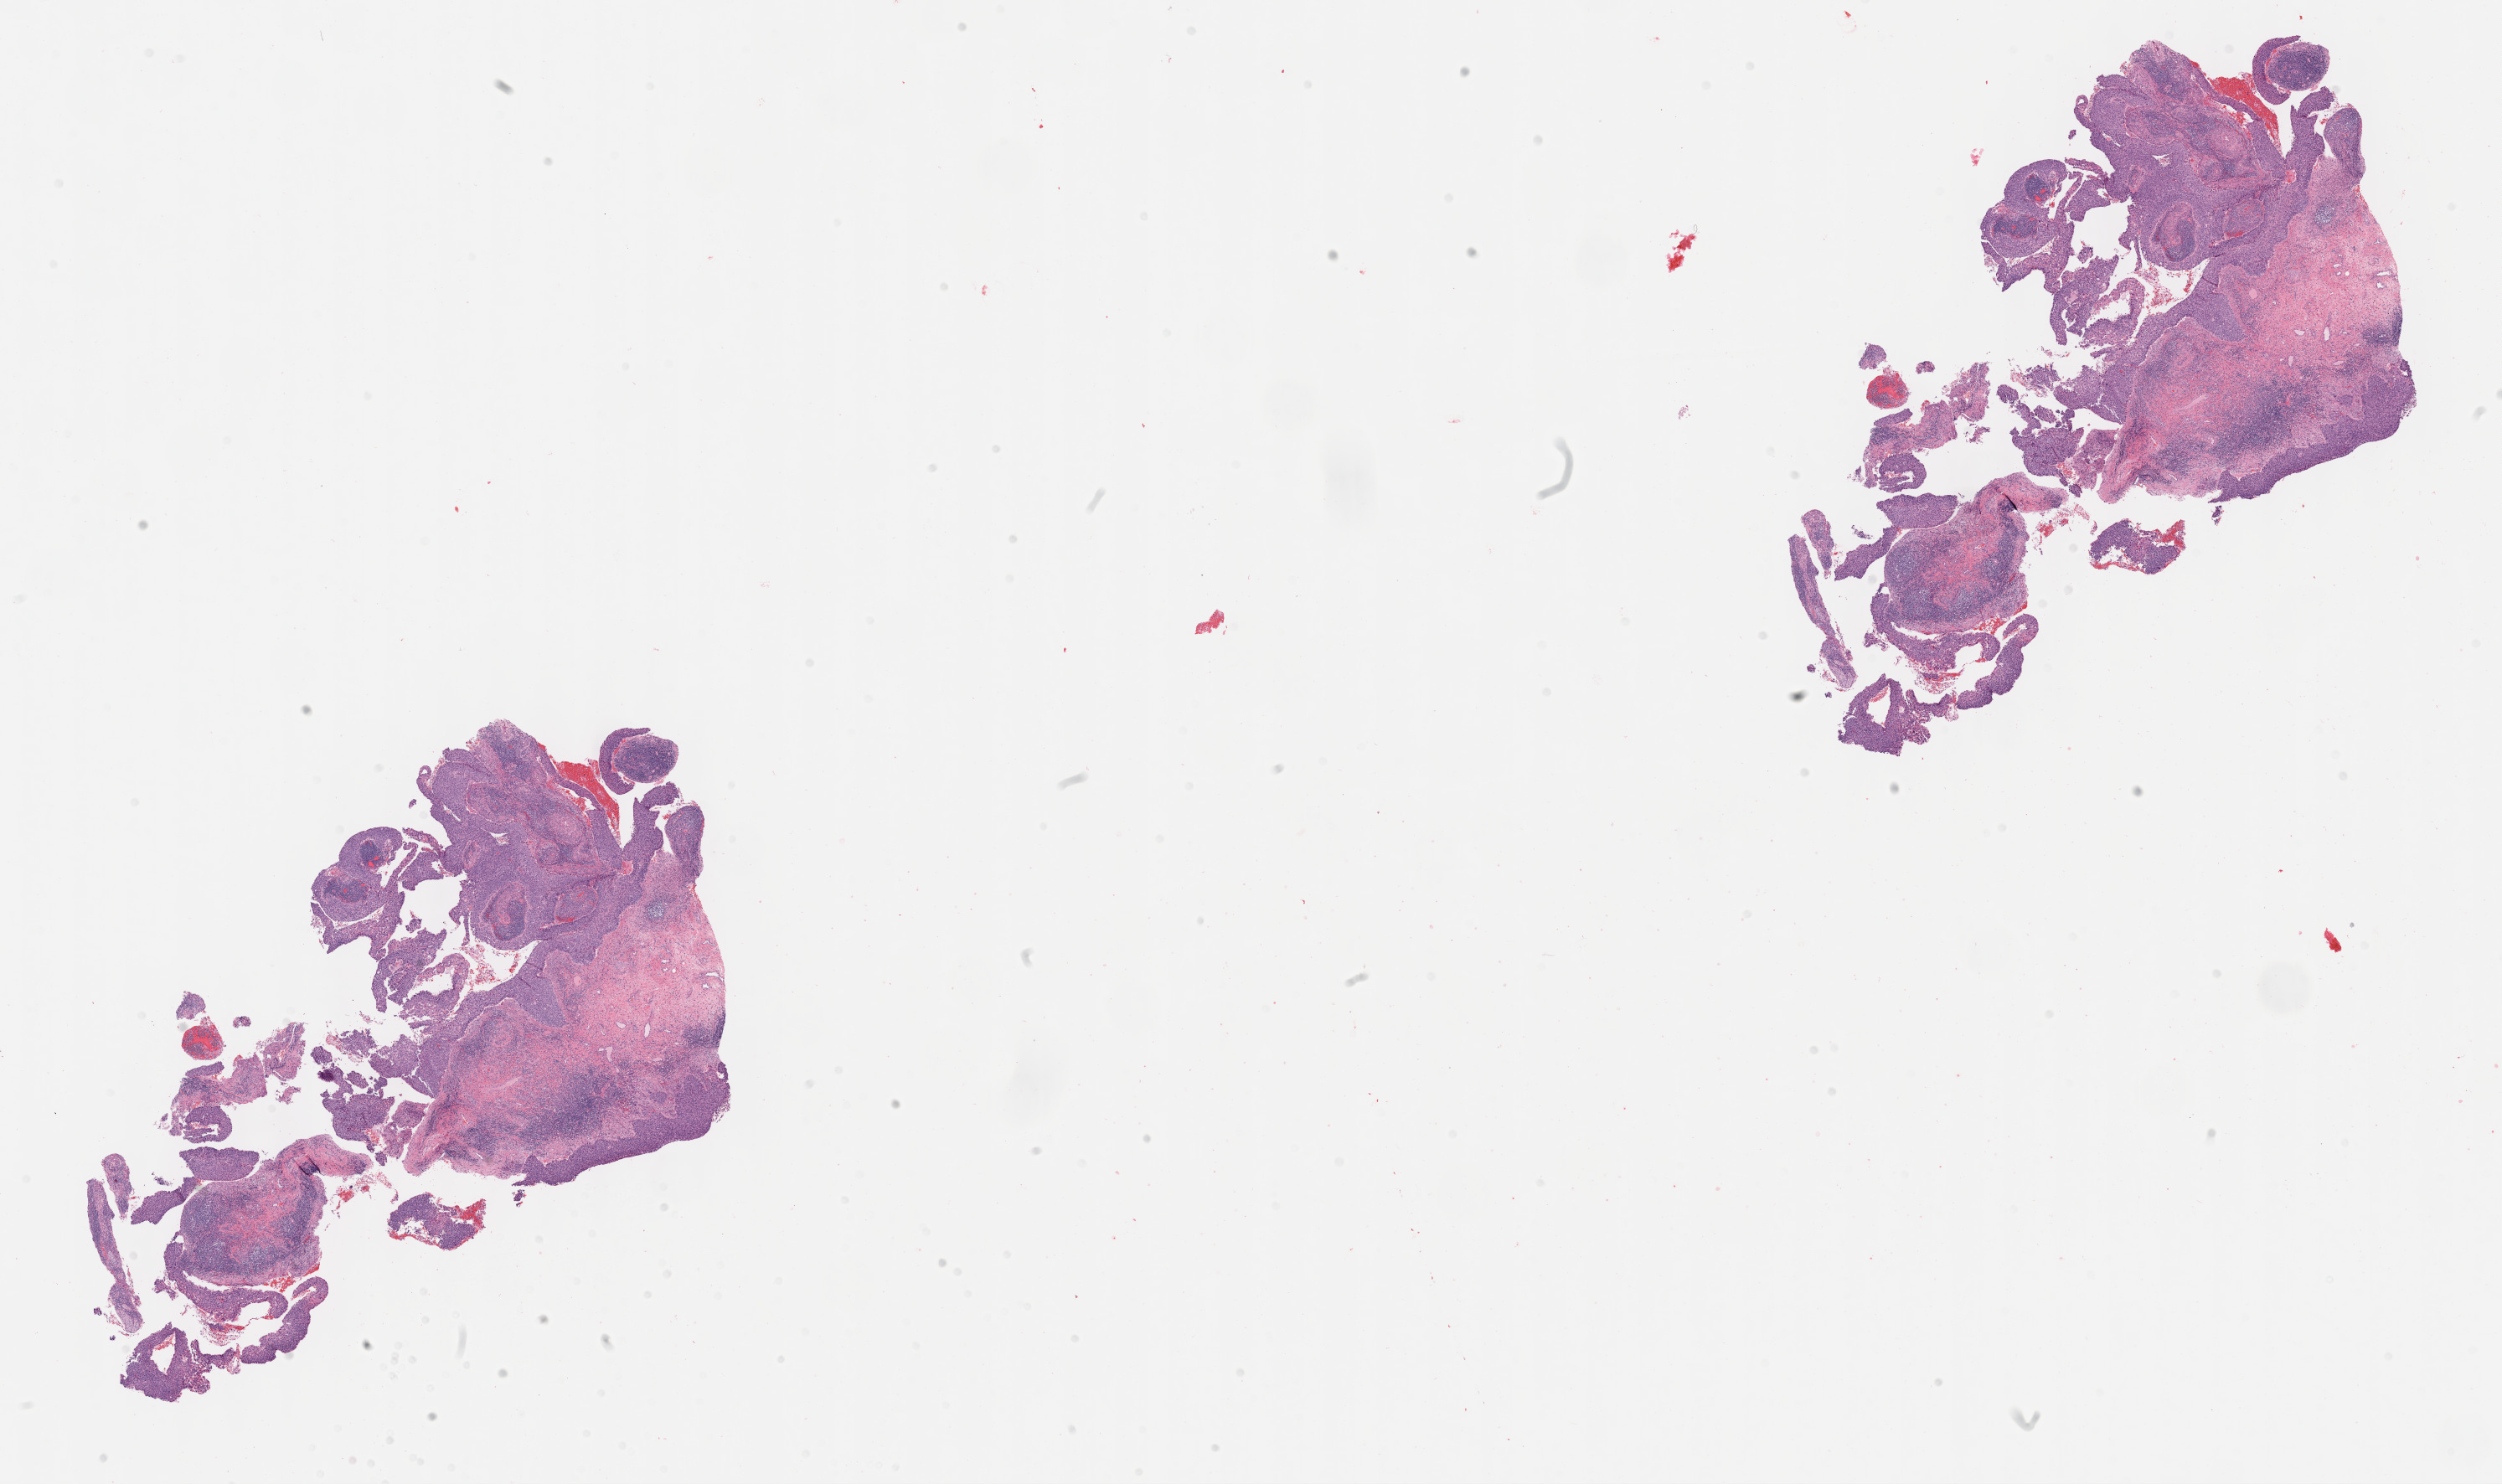
Digitized hematoxylin and eosin (H&E)-stained section, a low-resolution overview of the entire scanned area, about 24.2 x 14.3 mm. Tumor tissue. Anatomic site: cervix. Patient: female, age 49 years.
* histologic diagnosis: Papillary squamous cell carcinoma